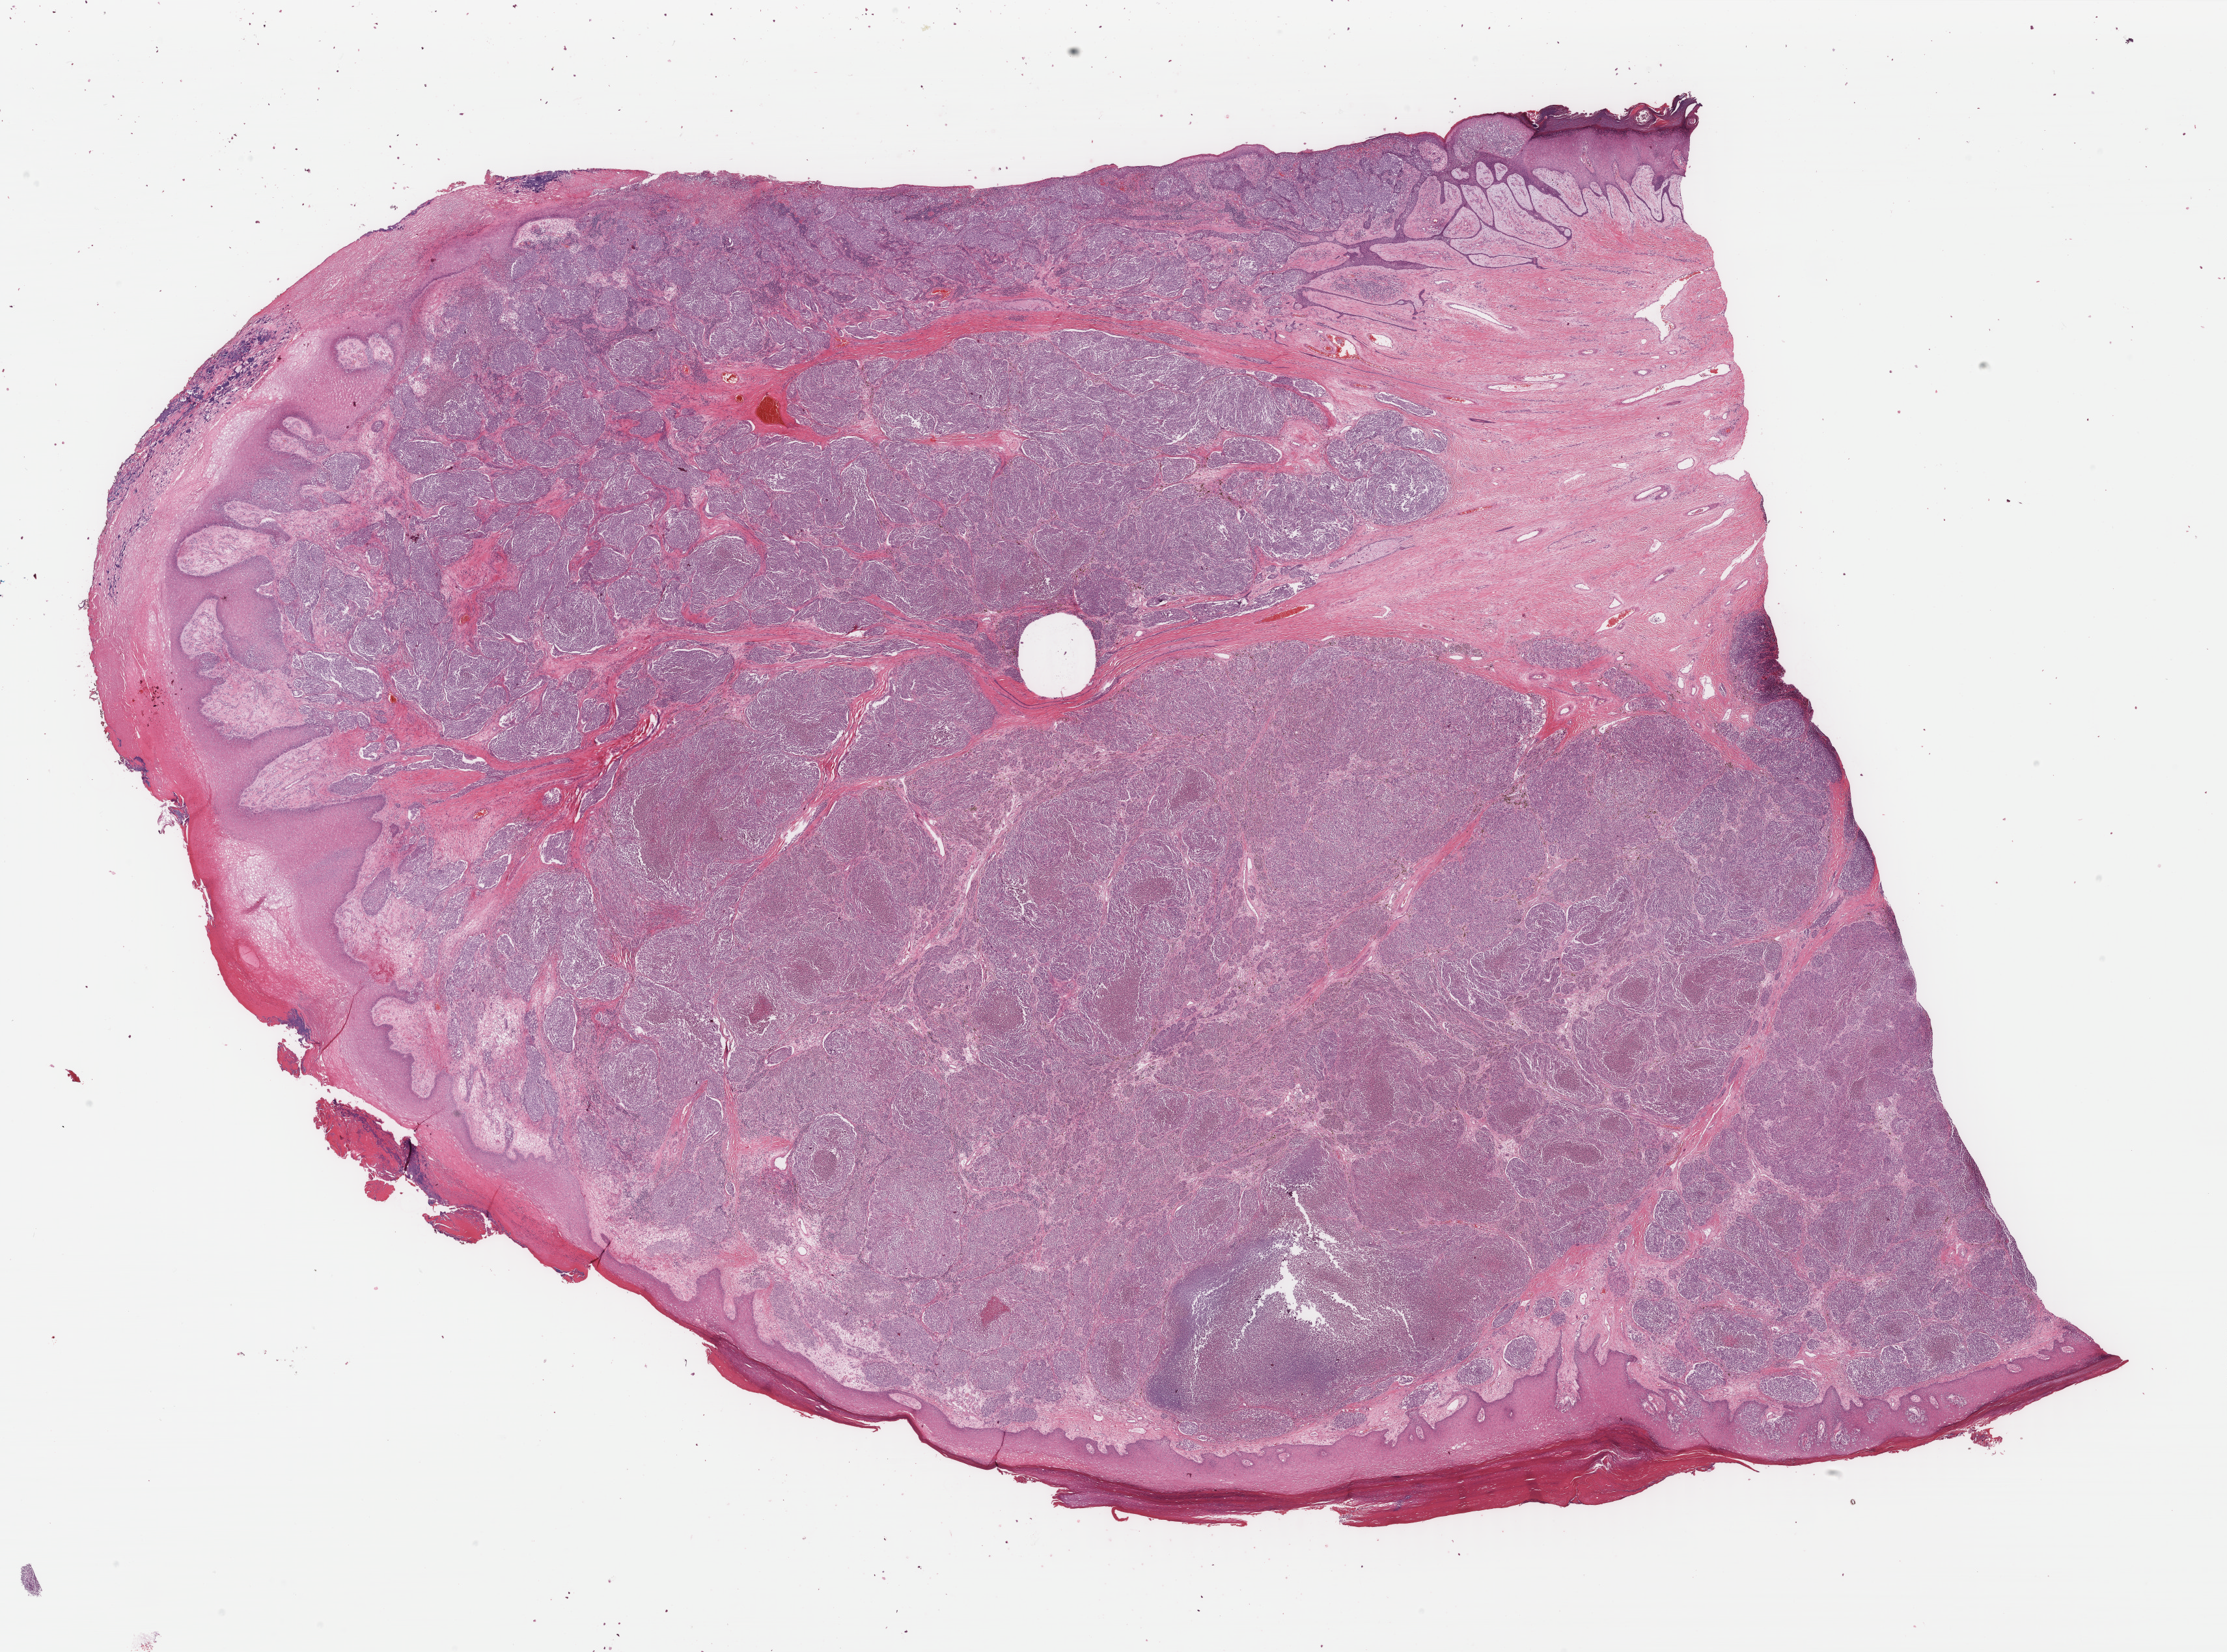
H&E whole-slide image — a low-resolution overview of the entire scanned area, about 27.2 x 20.1 mm. Formalin-fixed paraffin-embedded (FFPE) diagnostic section. Primary tumour sample from the skin. Patient: female, age at initial diagnosis 64 years.
- AJCC pathologic stage: IIC
- diagnosis: Acral lentiginous melanoma, malignant